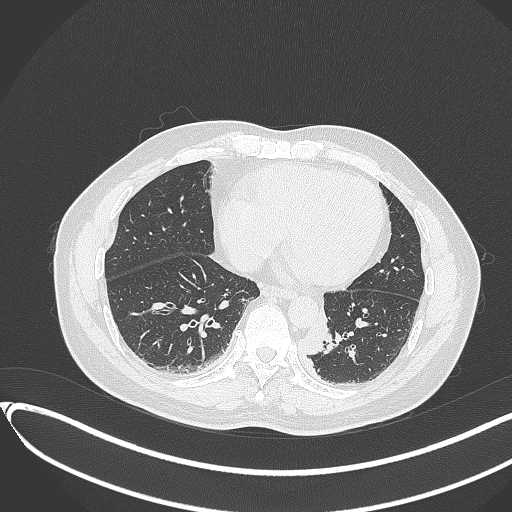
Chest CT, one axial slice. Position 110 of 417 along the scan axis. Lung window (W 1500 / L -600 HU). 512 × 512 image matrix, field of view 400 × 400 mm. Patient: male, 54 years. From the clinical record (not read from this slice): clinical TNM (as recorded): T3 N0 M0.
Annotated regions visible in this slice (rectangle marked by the reading radiologist):
- lung tumour (recorded histology: squamous cell carcinoma): bounding box <303,311,336,361> (left, top, right, bottom; pixels)